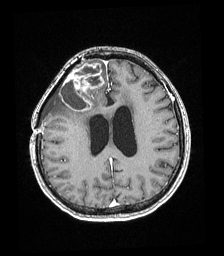
Brain MRI from a brain-tumour surgery series, one axial slice; position 76 of 192 along the scan axis; T1-weighted post-contrast; 224 × 256 image matrix. Case-level facts recorded for this patient, not image findings: histopathology: Astrocytoma; WHO grade: 4; IDH mutation: yes; tumour location: Right superficial frontal.
Structures marked on this image (outlined manually by an expert reader):
- tumour: bounding box [x1, y1, x2, y2] px = [59, 61, 104, 112]